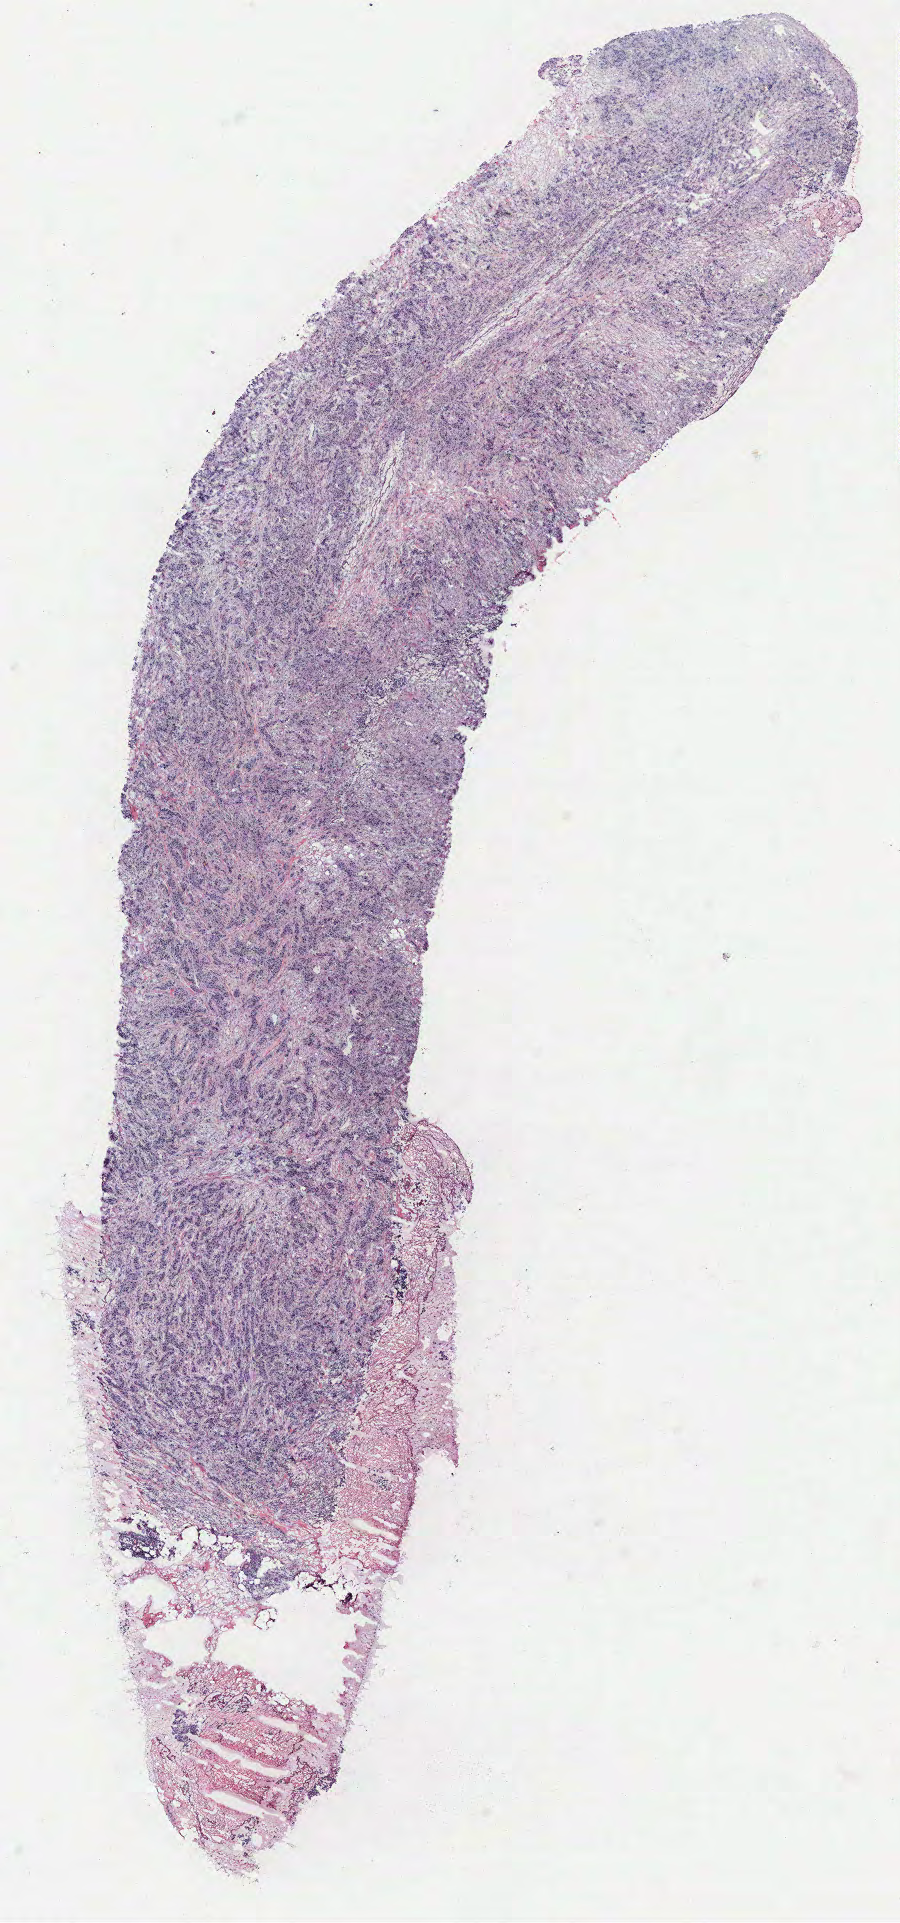
Digitized H&E tissue section (whole slide) — whole scanned area (about 7.2 x 15.4 mm) shown as a low-resolution overview, breast, tumour tissue. 45-year-old female patient.
AJCC pathologic stage: III. Histologic diagnosis: Infiltrating duct carcinoma, NOS.